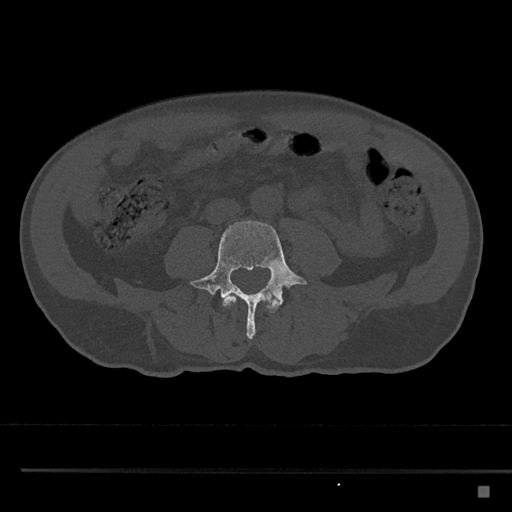
CT including the spine, one axial slice. Slice 643 of 797 in the series (ordered by position). Reconstruction kernel Br40s/3. 120 kVp. Bone window (W 1800 / L 400 HU). 0.5 mm slice thickness. 512 × 512 image matrix, field of view 391 × 391 mm. Patient: male, 59 years. From the clinical record (not read from this slice): primary cancer: prostate.
Annotated regions visible in this slice (semi-automatically segmented with operator editing):
- L3 vertebra: bounding box [x1, y1, x2, y2] px = [222, 293, 278, 313]
- L4 vertebra: [190, 220, 307, 339]